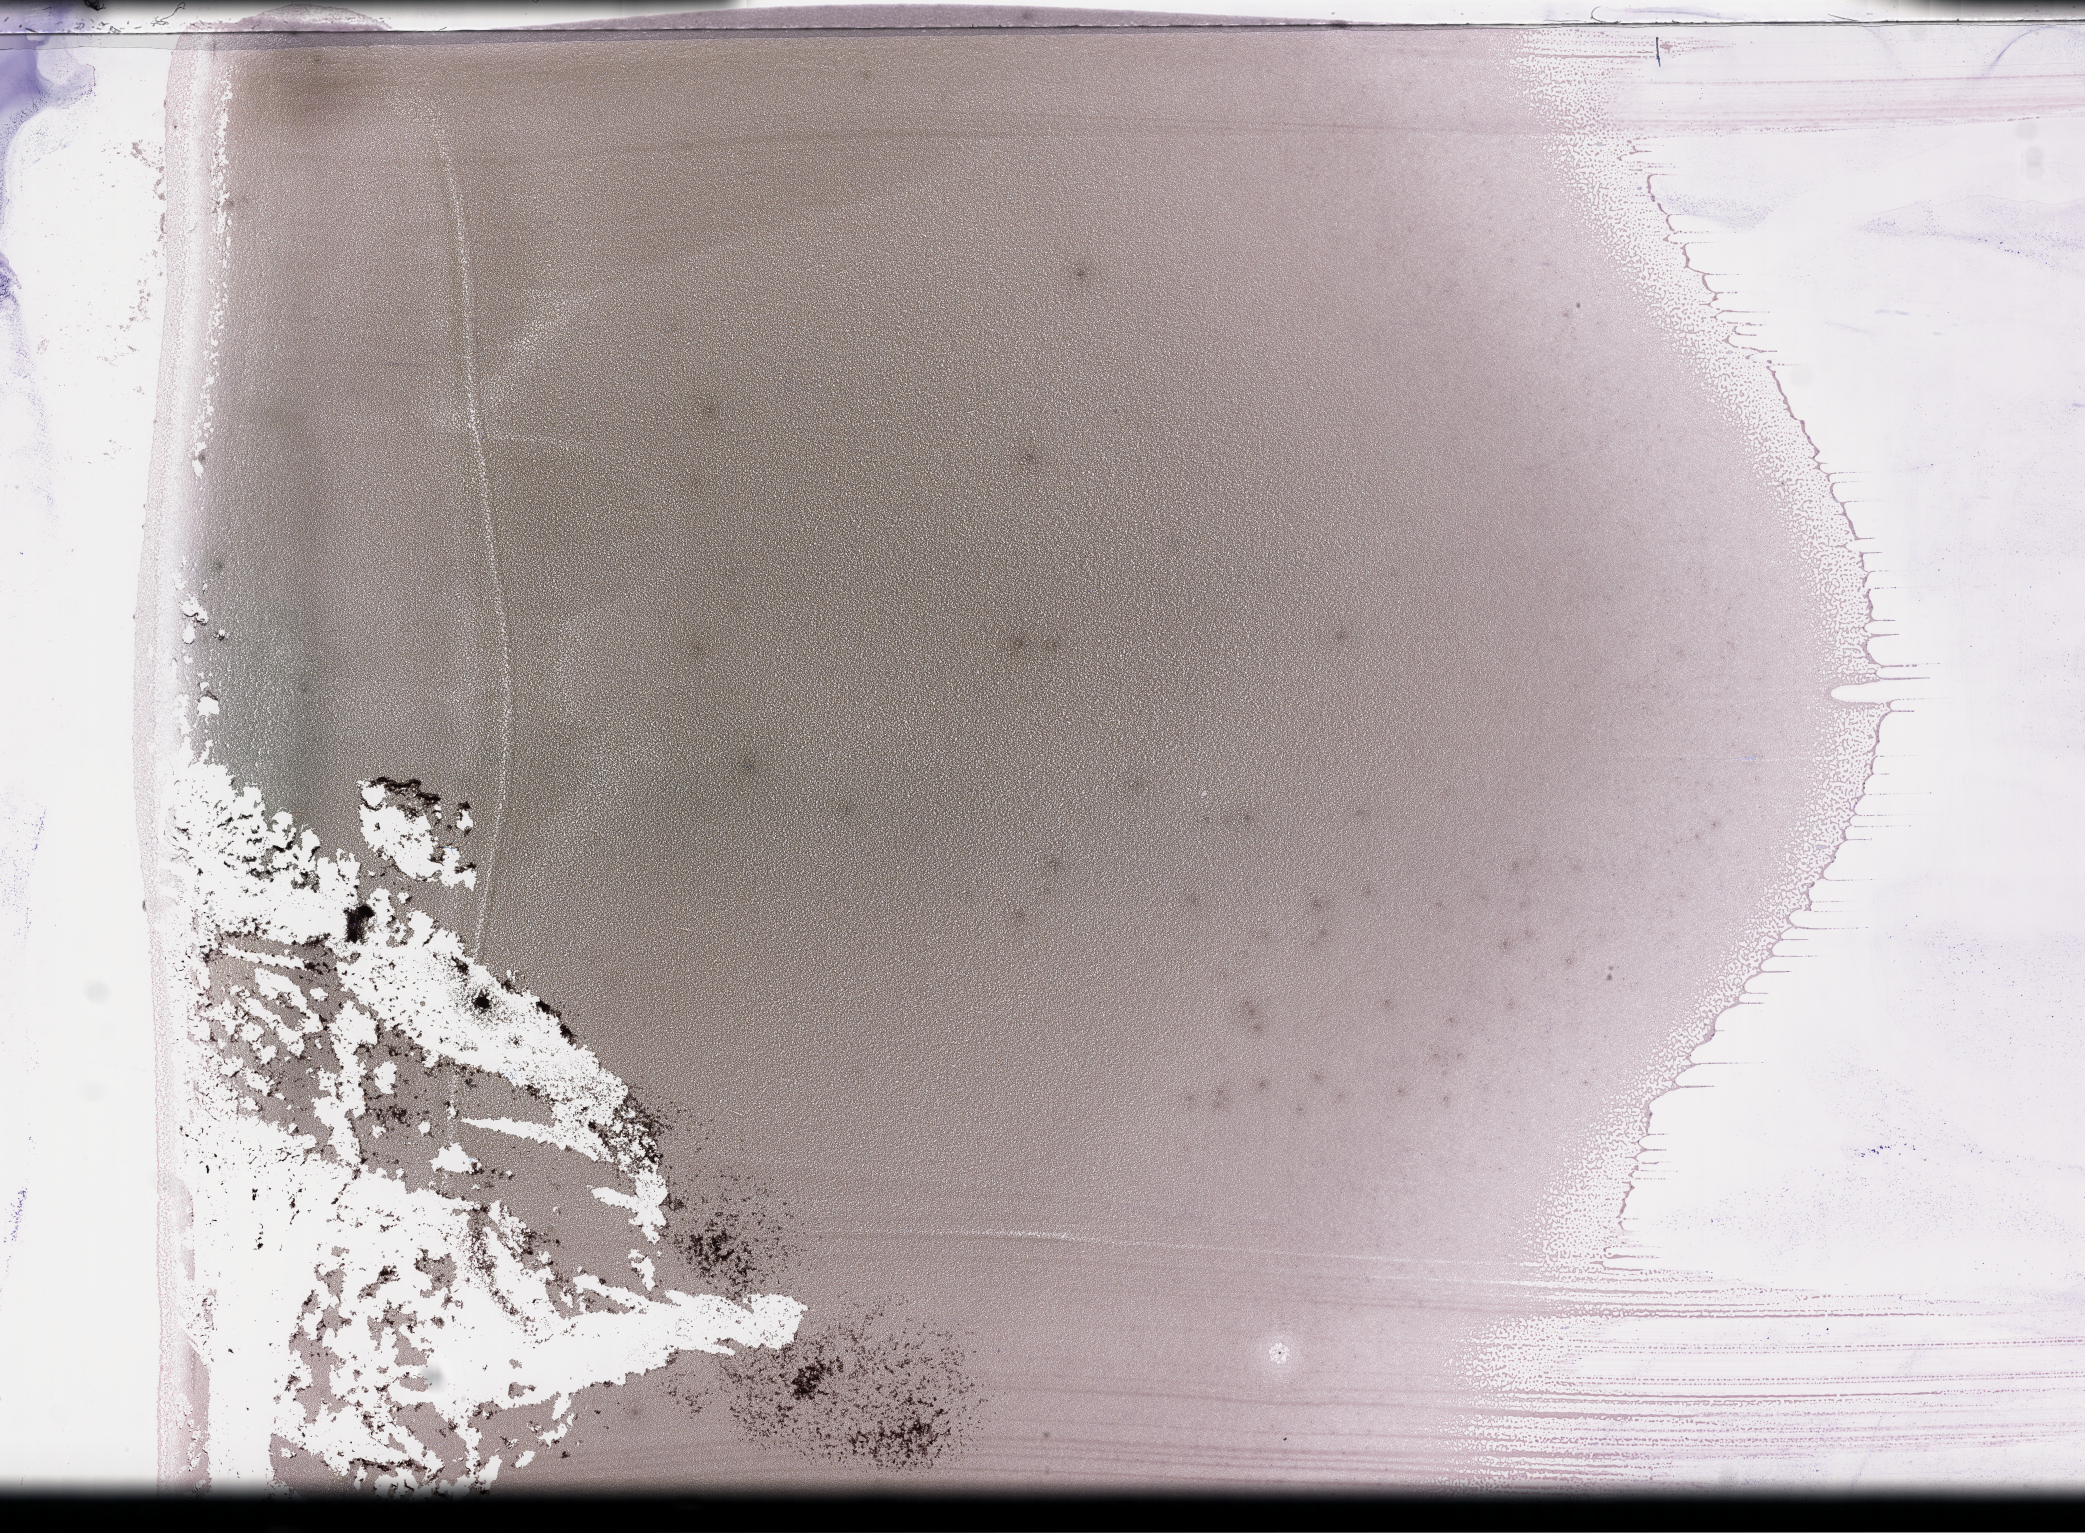
Whole-slide image of a whole blood smear, Wright–Giemsa stain — low-resolution overview of the scanned area, about 33.7 x 24.8 mm. Smear from an EDTA sample. Specimen time point: collected on treatment. Patient sex: female.
From a patient with: Plasma Cell Myeloma.